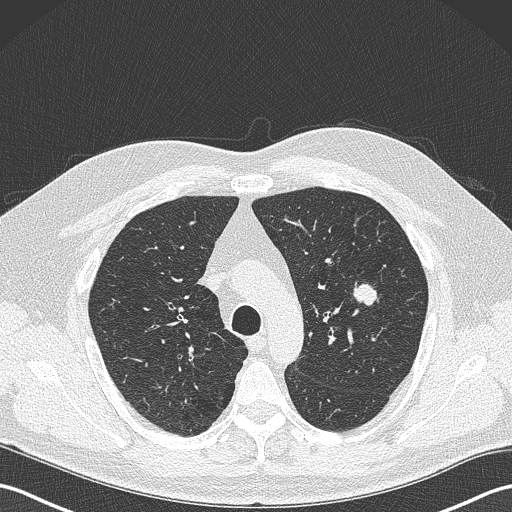
Axial slice from a low-dose chest CT screening exam, baseline screening round, lung window (W 1500 / L -600 HU), 1 mm slice thickness, slice 96 of 343 in the series, 512 × 512 image matrix, field of view 350 × 350 mm. Male participant, aged 61 years at enrolment. Former smoker at enrolment.
- Expert reader's lesion annotation, bounding box (x1, y1, x2, y2) in pixels: (344, 278, 385, 315).
- The screening reader recorded 2 non-calcified nodules or masses ≥4 mm on this exam (left upper lobe, lingula); which of them this box marks is not recorded.
- Official screen result: positive, change unspecified: nodule(s) >= 4 mm or enlarging nodule(s), mass(es), or other non-specific abnormalities suspicious for lung cancer.
- Lung cancer was diagnosed 160 days after this screen: adenocarcinoma, NOS, left upper lobe, poorly differentiated (G3), stage IA (AJCC 6th edition), 28 mm at pathology.